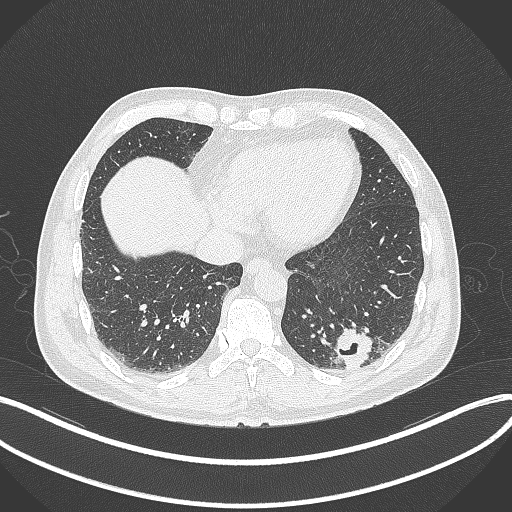
Chest CT, one axial slice; slice 76 of 300 in the series (ordered by position); 120 kVp; lung window (W 1500 / L -600 HU); 512 × 512 image matrix, field of view 400 × 400 mm. Patient: male, 54 years. Case-level facts recorded for this patient, not image findings: clinical TNM (as recorded): T1c N0 M1.
Structures marked on this image (rectangle marked by the reading radiologist):
- lung tumour (recorded histology: adenocarcinoma): box from (x=328, y=327) to (x=374, y=375) px